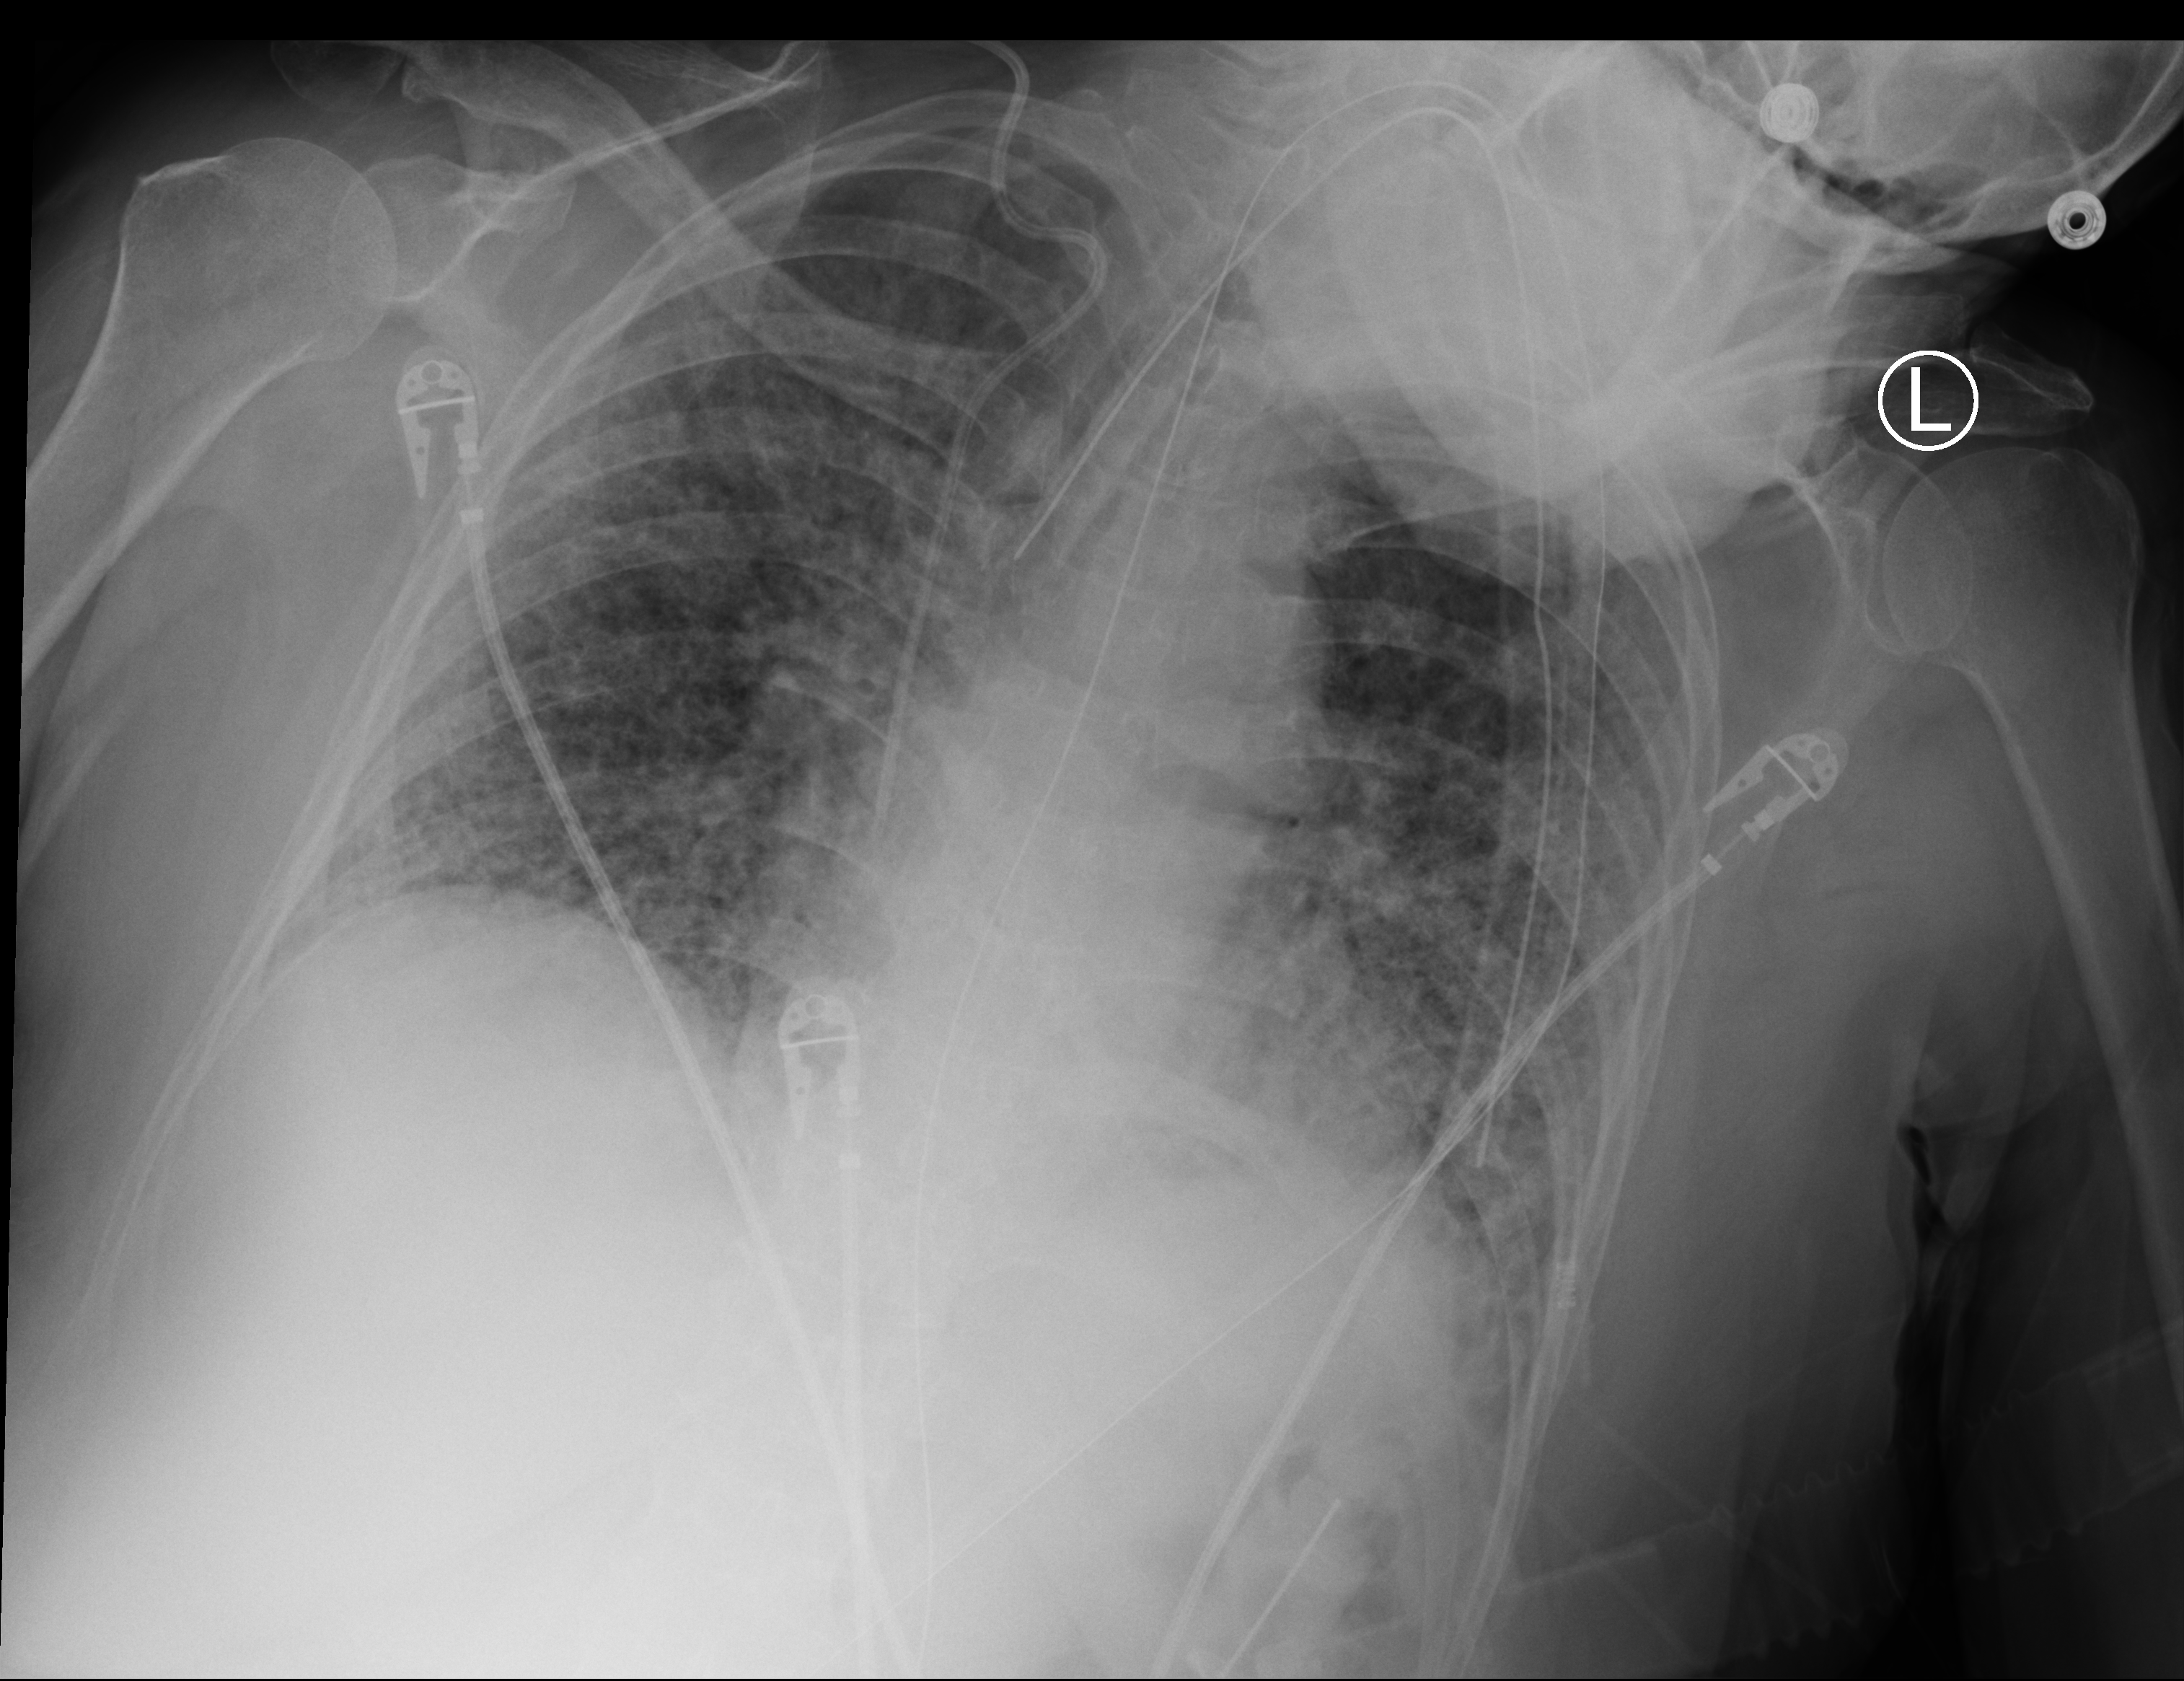
Portable chest radiograph, anteroposterior (AP) projection. Female patient hospitalised with COVID-19, age 60–74 years.
Hospital-stay facts (about this admission, not read from this image; timing relative to this image not recorded):
- mechanically ventilated during this hospital stay: yes